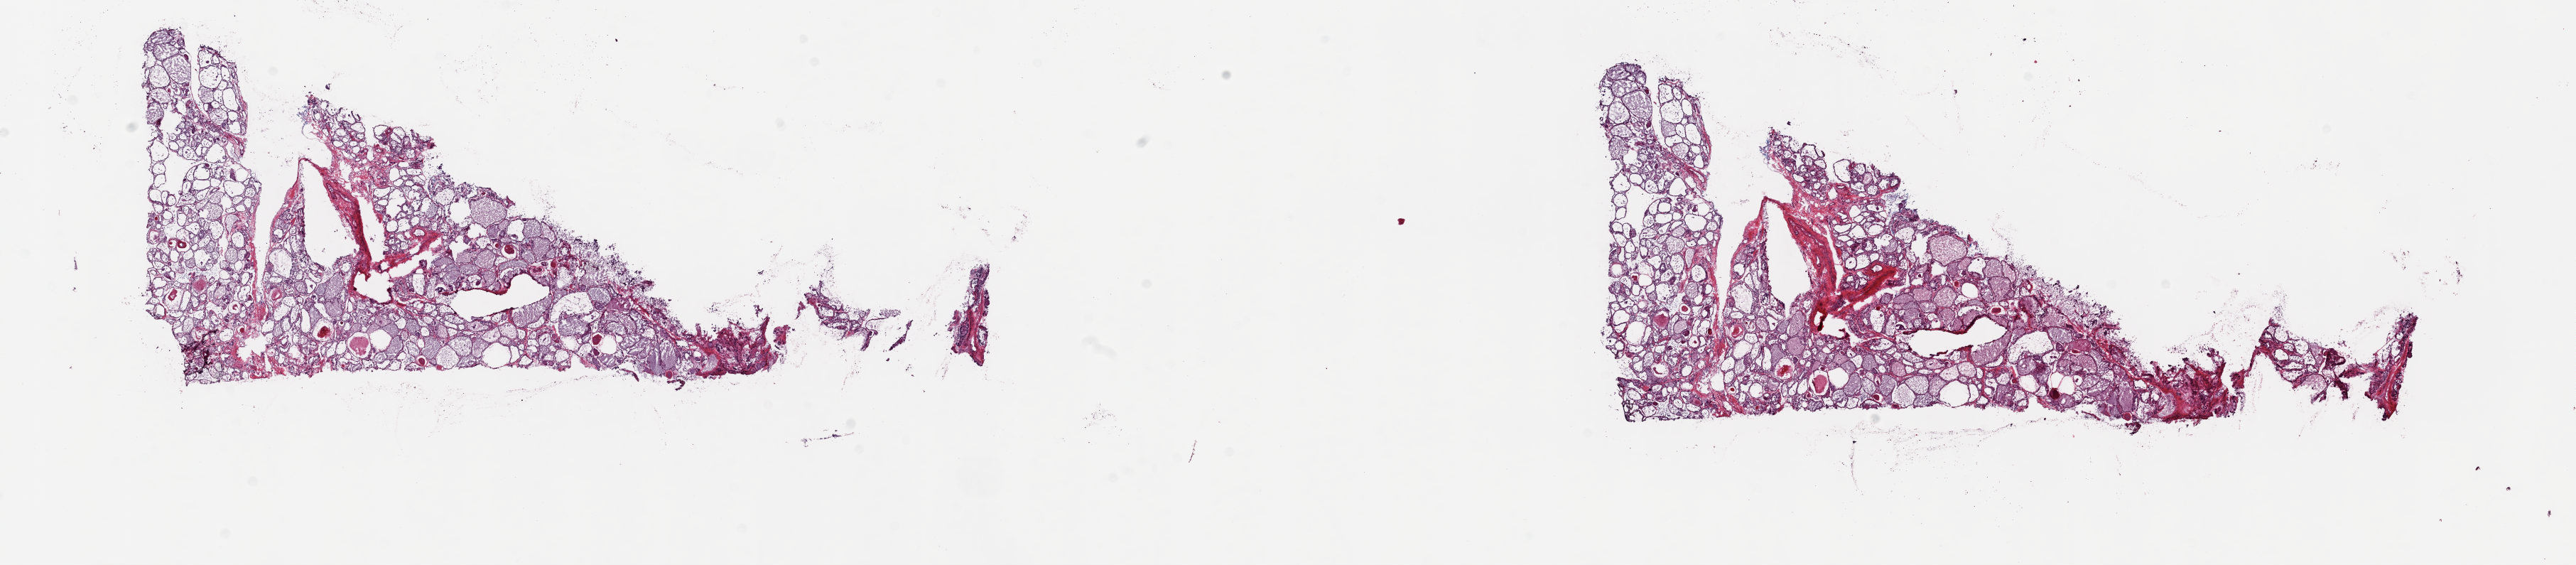
H&E whole-slide image — shown as a low-resolution overview of the whole scanned area (about 28.8 x 6.3 mm), frozen section, solid tissue normal (non-tumour tissue) sample from the thyroid. Male, age 52 years at initial diagnosis. Composition of this section per pathologist review: tumour cells 0%, tumour nuclei 0%, normal cells 60%, stromal cells 40%, necrosis 0%. Inflammatory infiltration, as recorded: lymphocyte infiltration 2%, monocyte infiltration 2%, neutrophil infiltration 1%.
This section: solid tissue normal sample (biorepository sample class). Patient diagnosis: Papillary adenocarcinoma, NOS (thyroid gland).